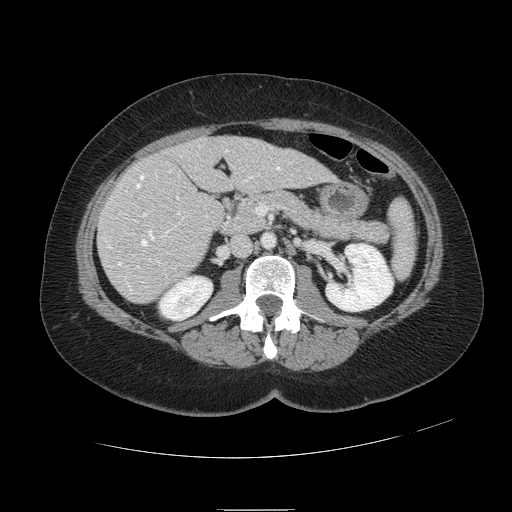
Contrast-enhanced abdominal CT, one axial slice. Position 41 of 121 along the scan axis. Intravenous contrast given. Soft-tissue window (W 400 / L 40 HU). 2.5 mm slice thickness. 512 × 512 image matrix, field of view 400 × 400 mm. Female patient, age 52 years. Case-level facts recorded for this patient, not image findings: diagnosis: colorectal cancer liver metastases, imaged before liver resection.
Structures marked on this image (manually delineated by an expert):
- hepatic veins: bounding box [x1, y1, x2, y2] px = [108, 151, 280, 266]
- liver: [99, 136, 333, 304]
- planned liver remnant (the part of the liver to remain after resection): [178, 136, 334, 194]
- portal vein (with intrahepatic branches): [138, 196, 180, 268]